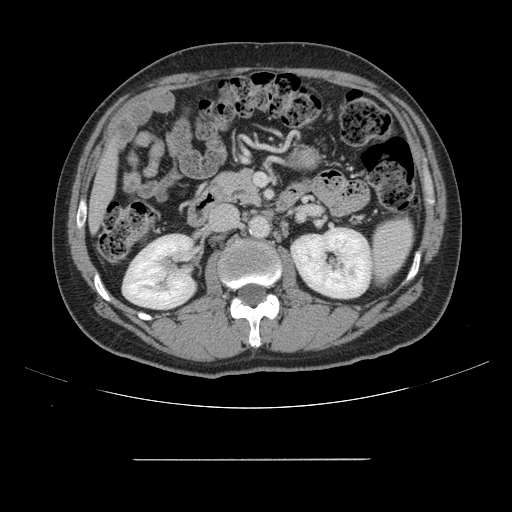
Contrast-enhanced abdominal CT, one axial slice. Position 58 of 164 along the scan axis. Intravenous contrast given. Soft-tissue window (W 400 / L 40 HU). 2.5 mm slice thickness. 512 × 512 image matrix, field of view 404 × 404 mm. Male patient, age 54 years. Case-level facts recorded for this patient, not image findings: diagnosis: colorectal cancer liver metastases, imaged before liver resection; multiple liver metastases: yes; largest metastasis: 1 cm; disease in both lobes: no.
Outlined on this slice (outlined manually by an expert reader):
- liver: bounding box [x1, y1, x2, y2] px = [91, 151, 115, 226]
- planned liver remnant (the part of the liver to remain after resection): [91, 151, 115, 226]